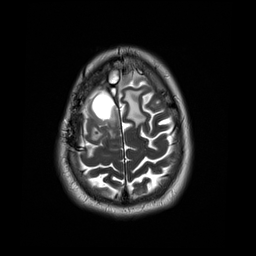
Brain MRI from a brain-tumour surgery series, one axial slice; slice 8 of 44 in the series (ordered by position); 256 × 256 image matrix, field of view 240 × 240 mm. Case-level facts recorded for this patient, not image findings: histopathology: Astrocytoma; WHO grade: 4.
Structures marked on this image (manually delineated by an expert):
- tumour: bounding box <92,107,119,139> (left, top, right, bottom; pixels)